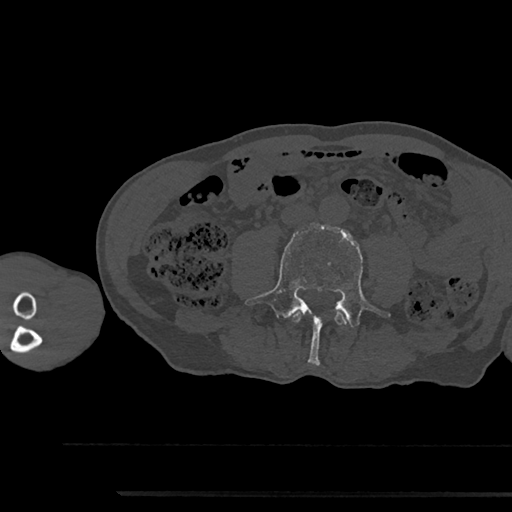
CT including the spine, one axial slice; position 427 of 797 along the scan axis; reconstruction kernel Br40s/3; bone window (W 1800 / L 400 HU); 512 × 512 image matrix. Male patient, age 79 years. From the clinical record (not read from this slice): primary cancer: prostate.
Annotated regions visible in this slice (semi-automatically segmented with operator editing):
- L3 vertebra: bounding box <293,312,347,325> (left, top, right, bottom; pixels)
- L4 vertebra: <244,224,391,365>